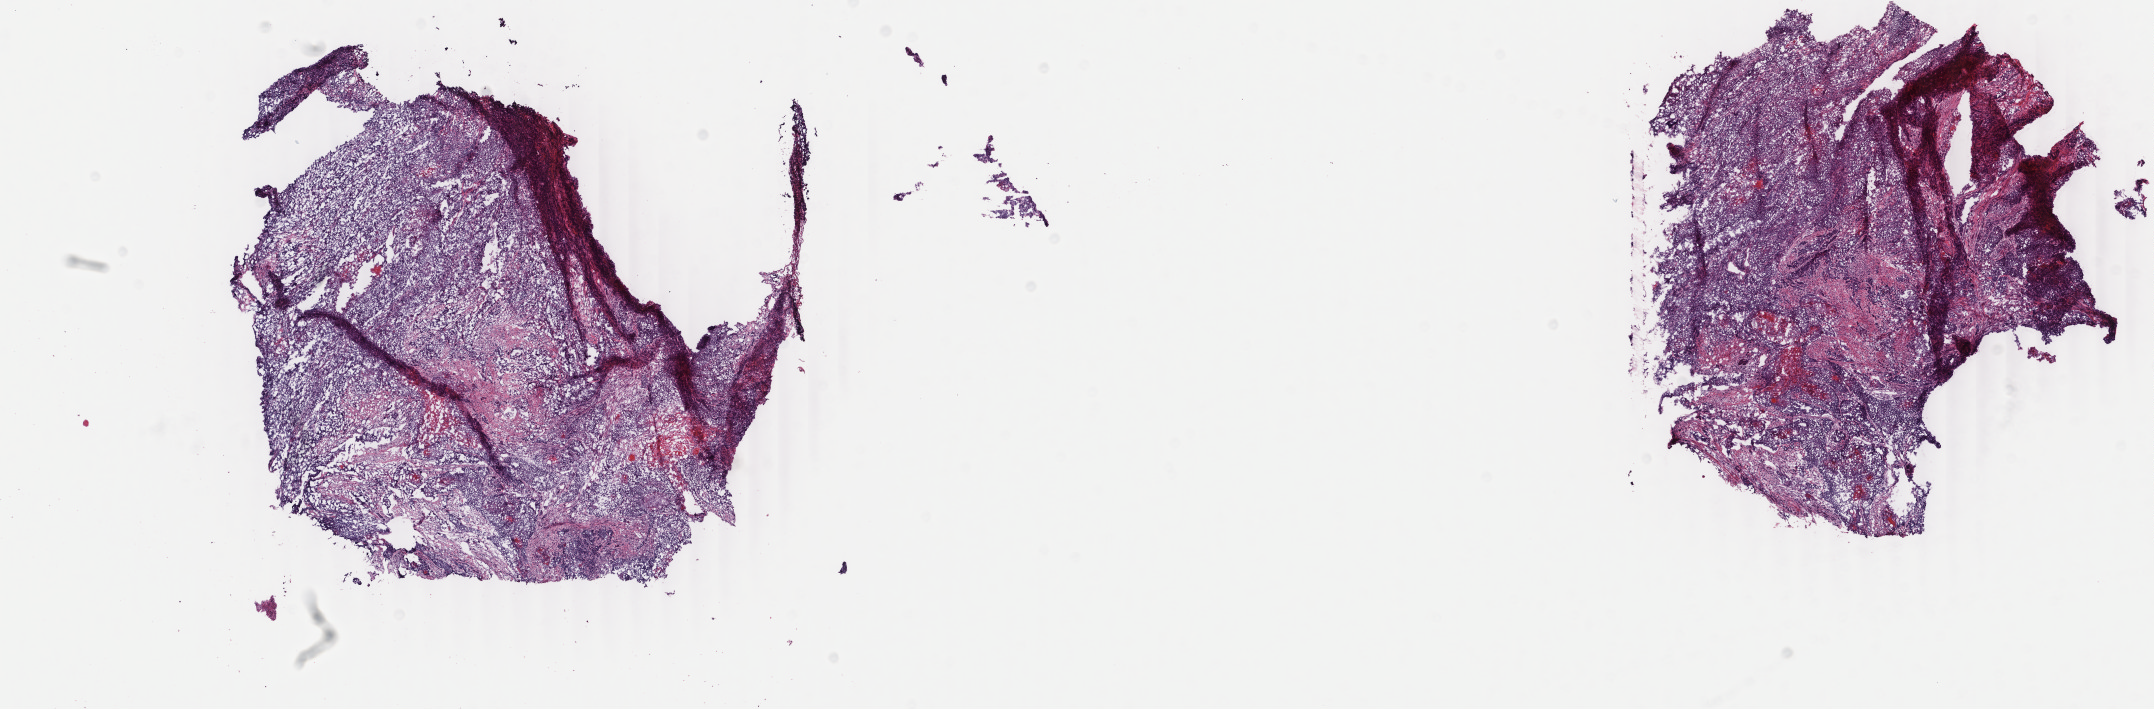
H&E-stained whole-slide image, a low-resolution overview of the entire scanned area, about 17.1 x 5.6 mm (acquisition: 40x scan); frozen section from the top of the tissue portion; primary tumour sample from the uterus. Female, age 54 years at initial diagnosis. Composition of this section per pathologist review: tumour cells 80%, tumour nuclei 90%.
Diagnosis: Endometrioid adenocarcinoma, NOS (endometrium).